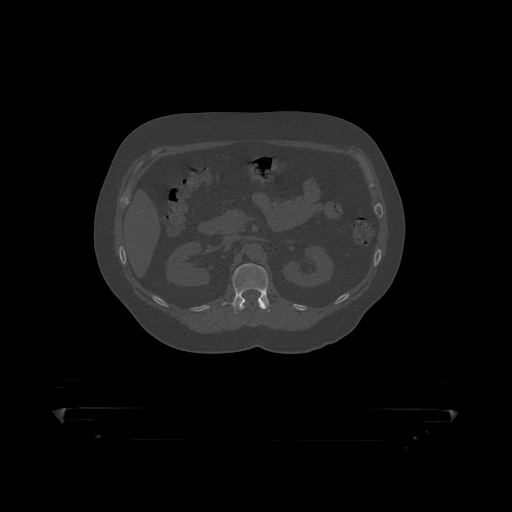
CT including the spine, one axial slice. Slice 153 of 390 in the series (ordered by position). Reconstruction kernel STANDARD. Bone window (W 1800 / L 400 HU). 1.25 mm slice thickness. 512 × 512 image matrix, field of view 650 × 650 mm. Male patient, age 60 years. From the clinical record (not read from this slice): primary cancer: prostate.
Structures marked on this image (semi-automatic segmentation, software-assisted and operator-edited):
- L1 vertebra: bounding box [x1, y1, x2, y2] px = [222, 263, 270, 315]
- T12 vertebra: [238, 300, 270, 312]